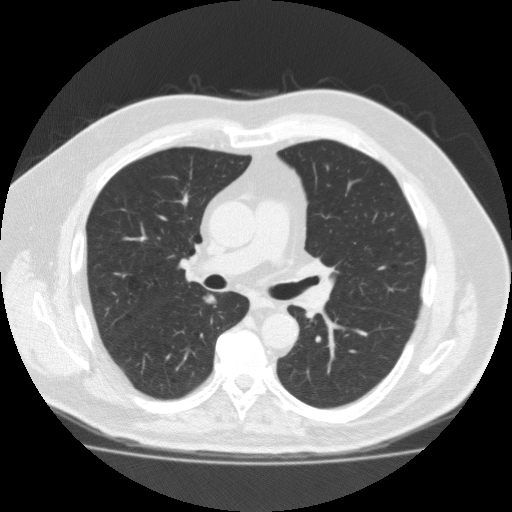
Low-dose screening chest CT, one axial slice; reconstruction kernel FC10; 120 kVp; lung window (W 1500 / L -600 HU); 2 mm slice thickness; 512 × 512 image matrix, field of view 391 × 391 mm.
Annotated regions visible in this slice (outlined manually by an expert reader):
- lesion 1 (tumor, lower lobe of right lung): bounding box [x1, y1, x2, y2] px = [207, 296, 214, 302]